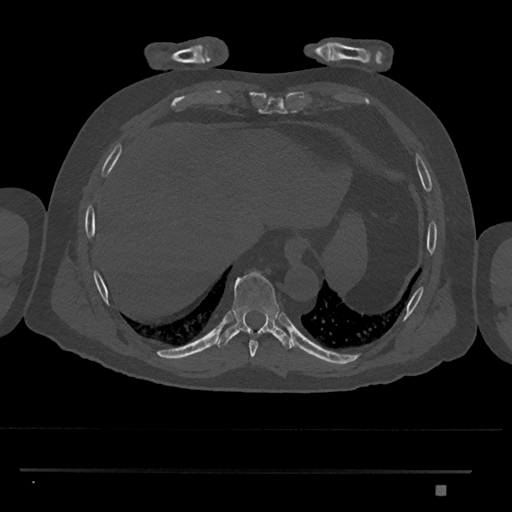
CT including the spine, one axial slice; slice 1073 of 1134 in the series (ordered by position); reconstruction kernel Br40s/3; bone window (W 1800 / L 400 HU); 512 × 512 image matrix, field of view 429 × 429 mm. Patient: male, 65 years. From the clinical record (not read from this slice): primary cancer: prostate.
Annotated regions visible in this slice (semi-automatic segmentation, software-assisted and operator-edited):
- T8 vertebra: bounding box [x1, y1, x2, y2] px = [249, 340, 258, 357]
- T9 vertebra: [216, 269, 293, 349]